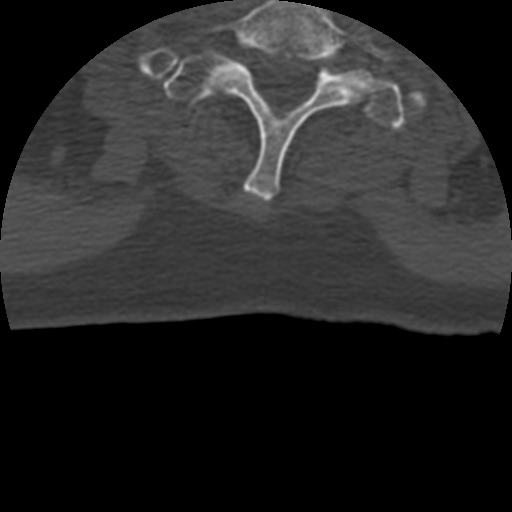
CT including the spine, one axial slice; position 391 of 399 along the scan axis; bone window (W 1800 / L 400 HU); 1.25 mm slice thickness; 512 × 512 image matrix. Patient age 69 years. From the clinical record (not read from this slice): primary cancer: prostate.
Annotated regions visible in this slice (semi-automatic segmentation, software-assisted and operator-edited):
- T1 vertebra: bounding box <159,51,407,130> (left, top, right, bottom; pixels)